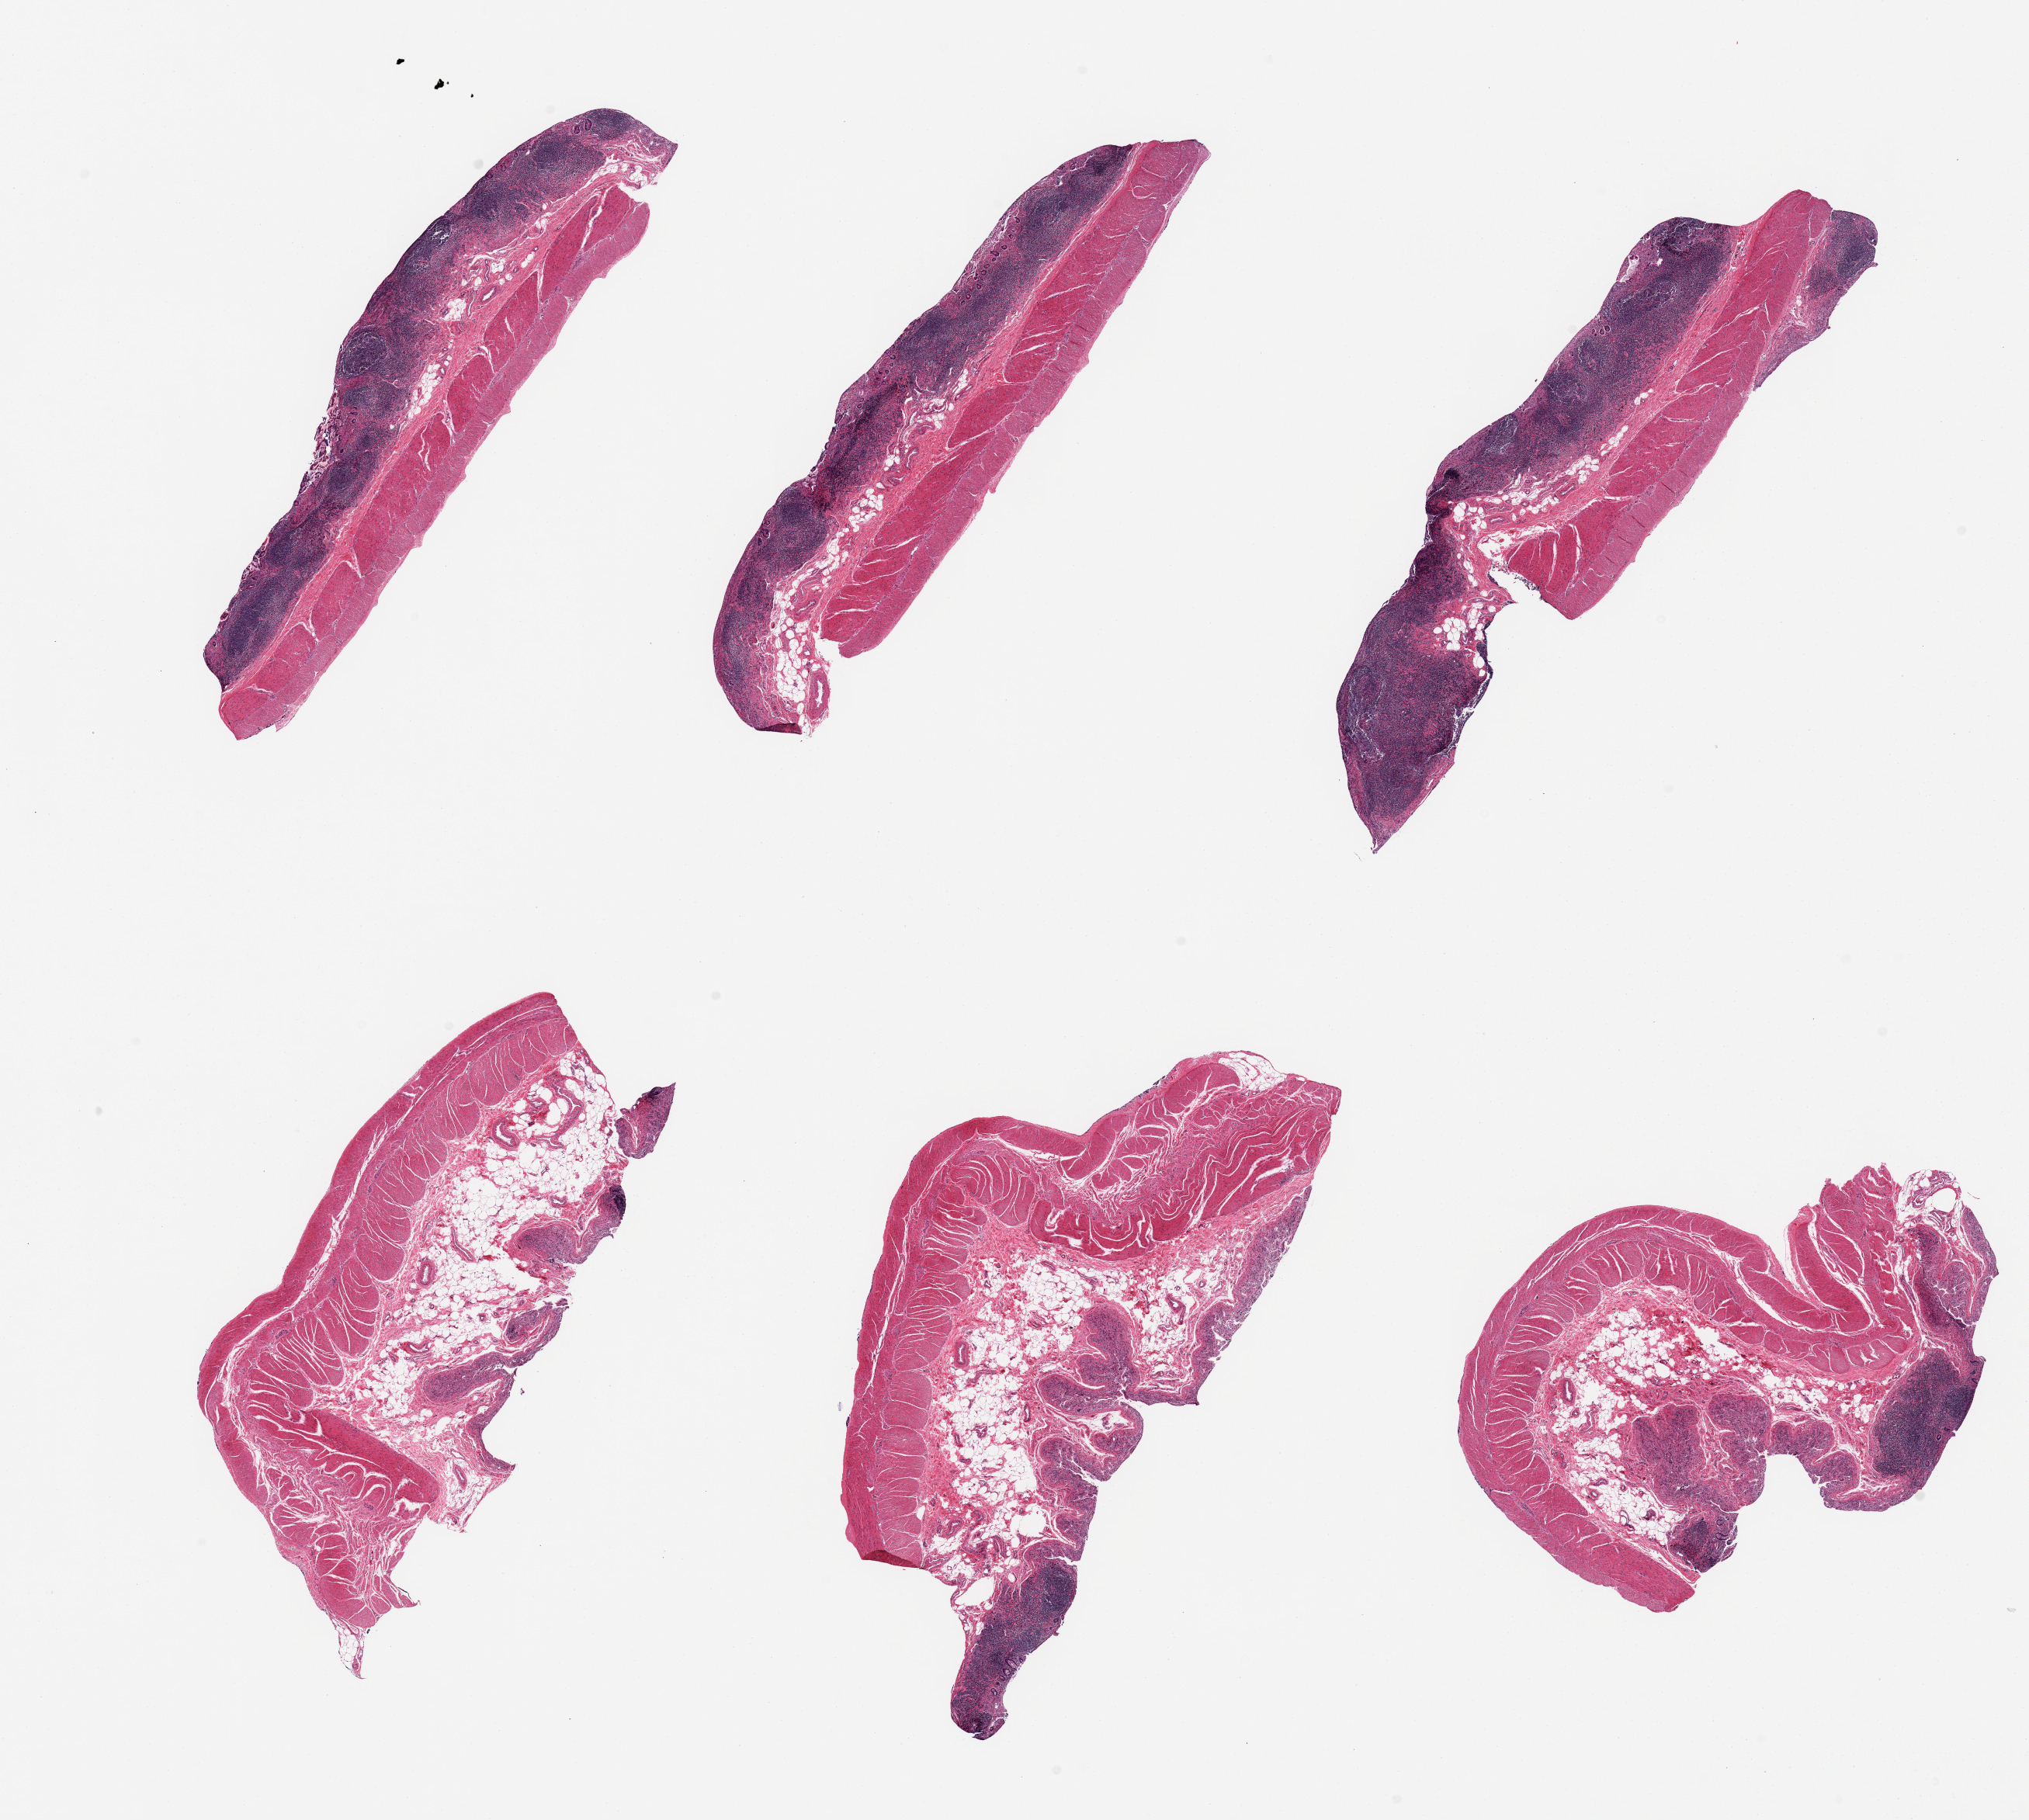
Whole-slide image, haematoxylin and eosin stain — a low-resolution overview of the entire scanned area, about 20.7 x 18.5 mm (from a 20x scan). PAXgene-fixed, paraffin-embedded tissue. Target tissue: ileum. Tissue donor sample. Male donor.
Review note (as recorded): 6 pieces, target lymphoid aggregates up to ~25% of tissue.